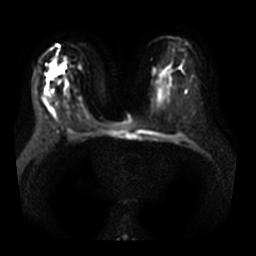
Breast MRI, one axial slice. Slice 19 of 32 in the series (ordered by position). Diffusion-weighted series; image 2 of 4 stored at this slice position (different b-values; order by instance number). 3 T. 5 mm slice thickness. 256 × 256 image matrix, field of view 350 × 350 mm. Female patient.
Annotated regions visible in this slice (outlined manually by an expert reader):
- tumour on diffusion-weighted imaging: bounding box (x1, y1, x2, y2) in pixels: (48, 68, 55, 79)